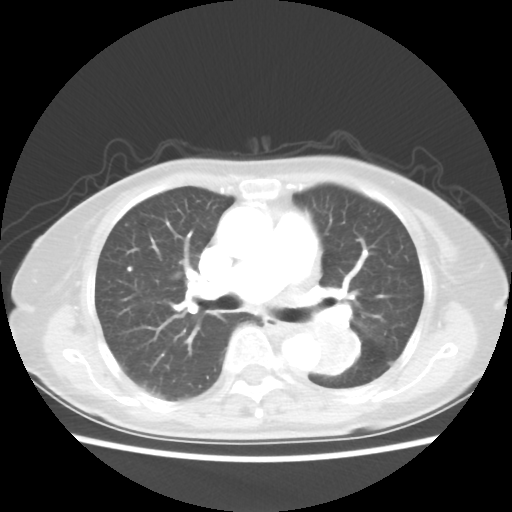
Chest CT, one axial slice; slice 29 of 50 in the series (ordered by position); reconstruction kernel STANDARD; 80 kVp; lung window (W 1500 / L -600 HU); 512 × 512 image matrix, field of view 335 × 335 mm. Female patient, age 81 years. Case-level facts recorded for this patient, not image findings: clinical TNM (as recorded): T2 N0 M1a.
Structures marked on this image (rectangle marked by the reading radiologist):
- lung tumour (recorded histology: squamous cell carcinoma): bounding box (x1, y1, x2, y2) in pixels: (304, 314, 366, 380)